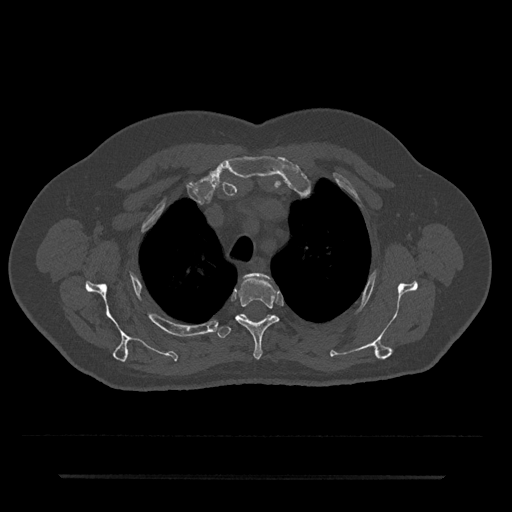
CT including the spine, one axial slice. Reconstruction kernel Br40s/3. 120 kVp. Bone window (W 1800 / L 400 HU). 0.5 mm slice thickness. 512 × 512 image matrix, field of view 437 × 437 mm. Patient: male, 69 years. Case-level facts recorded for this patient, not image findings: primary cancer: prostate.
Outlined on this slice (semi-automatic segmentation, software-assisted and operator-edited):
- T2 vertebra: bounding box [x1, y1, x2, y2] px = [247, 274, 269, 279]
- T3 vertebra: [235, 277, 279, 360]
- T4 vertebra: [218, 315, 246, 338]